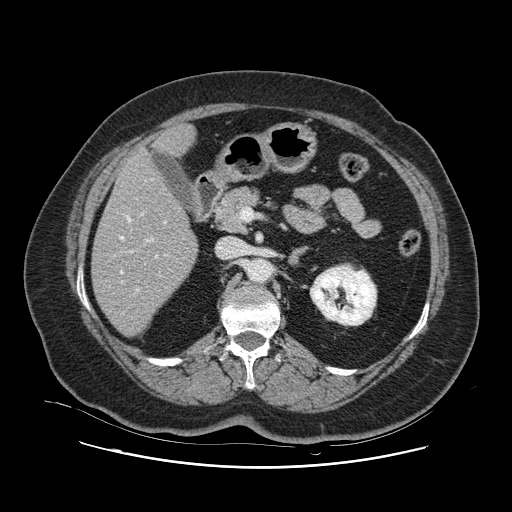
Contrast-enhanced abdominal CT, one axial slice. Slice 49 of 132 in the series (ordered by position). 120 kVp. Intravenous contrast given. Soft-tissue window (W 400 / L 40 HU). 2.5 mm slice thickness. 512 × 512 image matrix. Female patient, age 73 years. From the clinical record (not read from this slice): diagnosis: colorectal cancer liver metastases, imaged before liver resection; multiple liver metastases: no; largest metastasis: 7 cm; chemotherapy before resection: yes.
Outlined on this slice (manually delineated by an expert):
- hepatic veins: bounding box [x1, y1, x2, y2] px = [120, 178, 180, 283]
- liver: [93, 126, 198, 336]
- planned liver remnant (the part of the liver to remain after resection): [93, 152, 198, 336]
- portal vein (with intrahepatic branches): [136, 222, 166, 292]